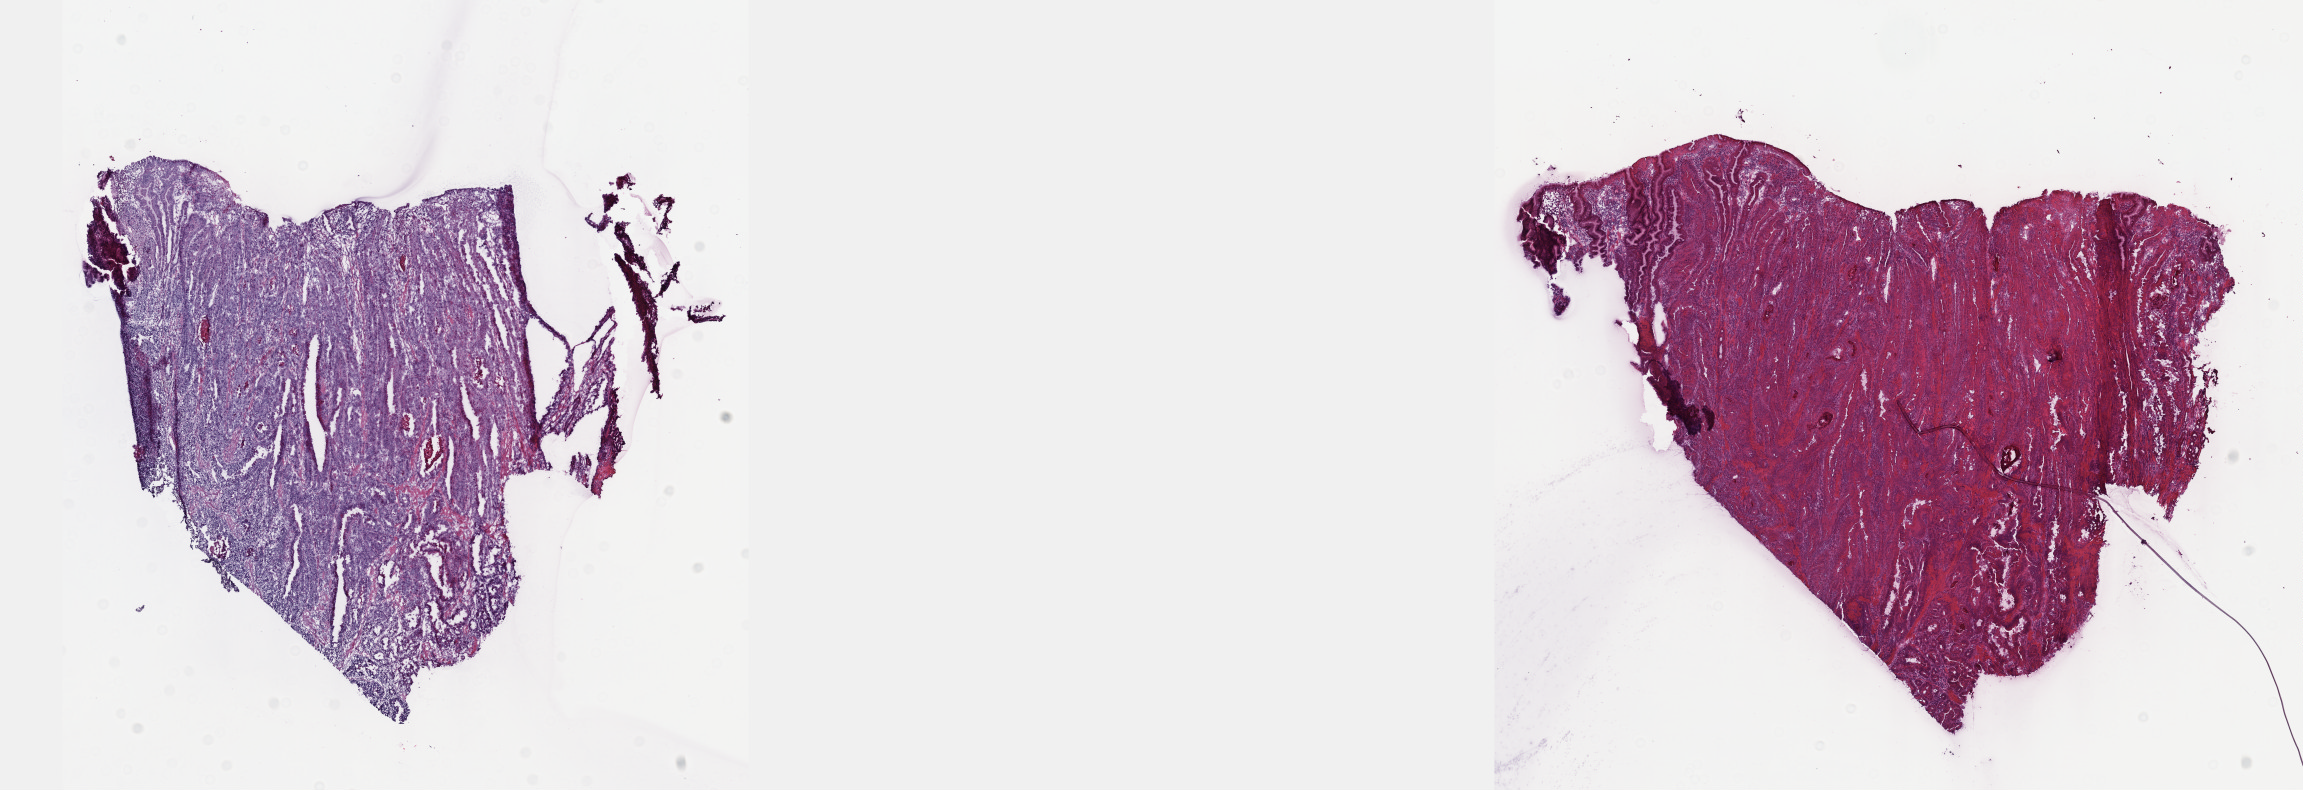
Whole-slide histology image, H&E, a low-resolution overview of the entire scanned area, about 18.6 x 6.4 mm (slide scanned at 40x). Frozen section from the top of the tissue portion. Sample: primary tumour, stomach. Female patient; age at initial diagnosis 59 years. Histologic grade: G2 (moderately differentiated). Pathologist review of this section (percent, as recorded): tumour cells 75%, tumour nuclei 90%, normal cells 0%, stromal cells 22%, necrosis 3%. Inflammatory infiltration, as recorded: lymphocyte infiltration 5%, monocyte infiltration 1%, neutrophil infiltration 1%.
Lymph nodes positive (case pathology): 18 of 32 examined. AJCC pathologic stage: IV. Diagnosis: Tubular adenocarcinoma (gastric antrum).